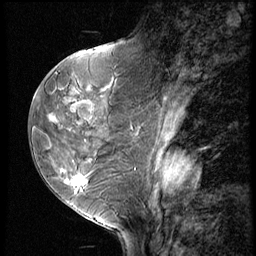
Breast MRI (dynamic contrast-enhanced), one sagittal slice; slice 28 of 60 in the series (ordered by position); 3 images stored at this slice position (order not interpretable as contrast timing); 1.5 T; TE 4.2 ms, TR 8.9 ms; 2.5 mm slice thickness; 256 × 256 image matrix. Patient: female, 50 years. Case-level facts recorded for this patient, not image findings: setting: breast cancer imaged before/during neoadjuvant chemotherapy; receptor status: HR-positive, HER2-negative.
Structures marked on this image (semi-automatic segmentation, software-assisted and operator-edited):
- analysis volume of interest (the breast-tissue region the enhancement analysis was run in; not a lesion): bounding box [x1, y1, x2, y2] px = [38, 102, 118, 213]
- tumour enhancement mask (voxels above the 140 % enhancement threshold inside the analysis volume of interest): [63, 170, 88, 187]